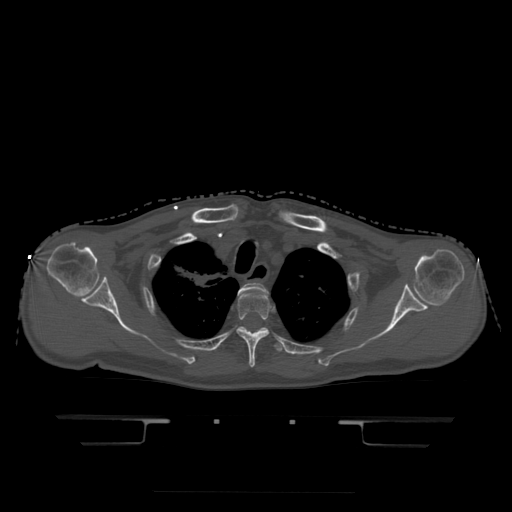
CT including the spine, one axial slice. Position 369 of 522 along the scan axis. Bone window (W 1800 / L 400 HU). 1.25 mm slice thickness. 512 × 512 image matrix. Patient age 68 years. Case-level facts recorded for this patient, not image findings: primary cancer: urothelial.
Outlined on this slice (semi-automatically segmented with operator editing):
- T2 vertebra: bounding box <239,283,269,294> (left, top, right, bottom; pixels)
- T3 vertebra: <237,288,270,368>
- T4 vertebra: <220,327,283,353>